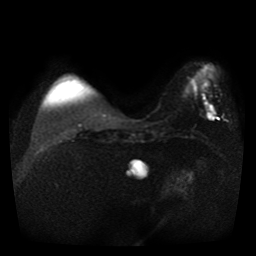
Breast MRI, one axial slice; position 10 of 41 along the scan axis; diffusion-weighted series; image 2 of 4 stored at this slice position (different b-values; order by instance number); 1.5 T; 256 × 256 image matrix. Female patient.
Outlined on this slice (outlined manually by an expert reader):
- tumour on diffusion-weighted imaging: box from (x=208, y=114) to (x=213, y=119) px